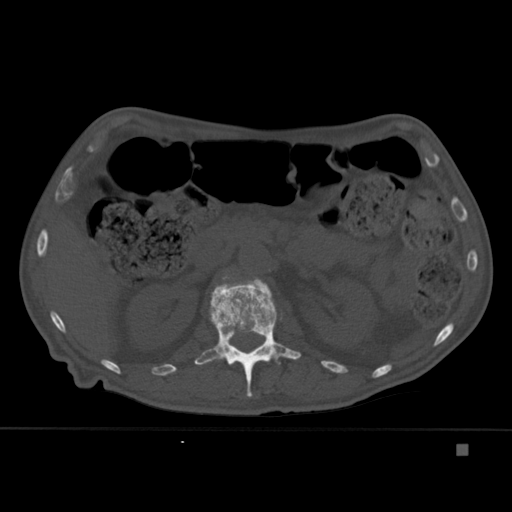
CT including the spine, one axial slice; slice 181 of 451 in the series (ordered by position); bone window (W 1800 / L 400 HU); 1.5 mm slice thickness; 512 × 512 image matrix, field of view 378 × 378 mm. Male patient, age 75 years. From the clinical record (not read from this slice): primary cancer: prostate.
Annotated regions visible in this slice (semi-automatically segmented with operator editing):
- L1 vertebra: bounding box [x1, y1, x2, y2] px = [194, 278, 301, 397]
- L2 vertebra: [222, 276, 229, 280]